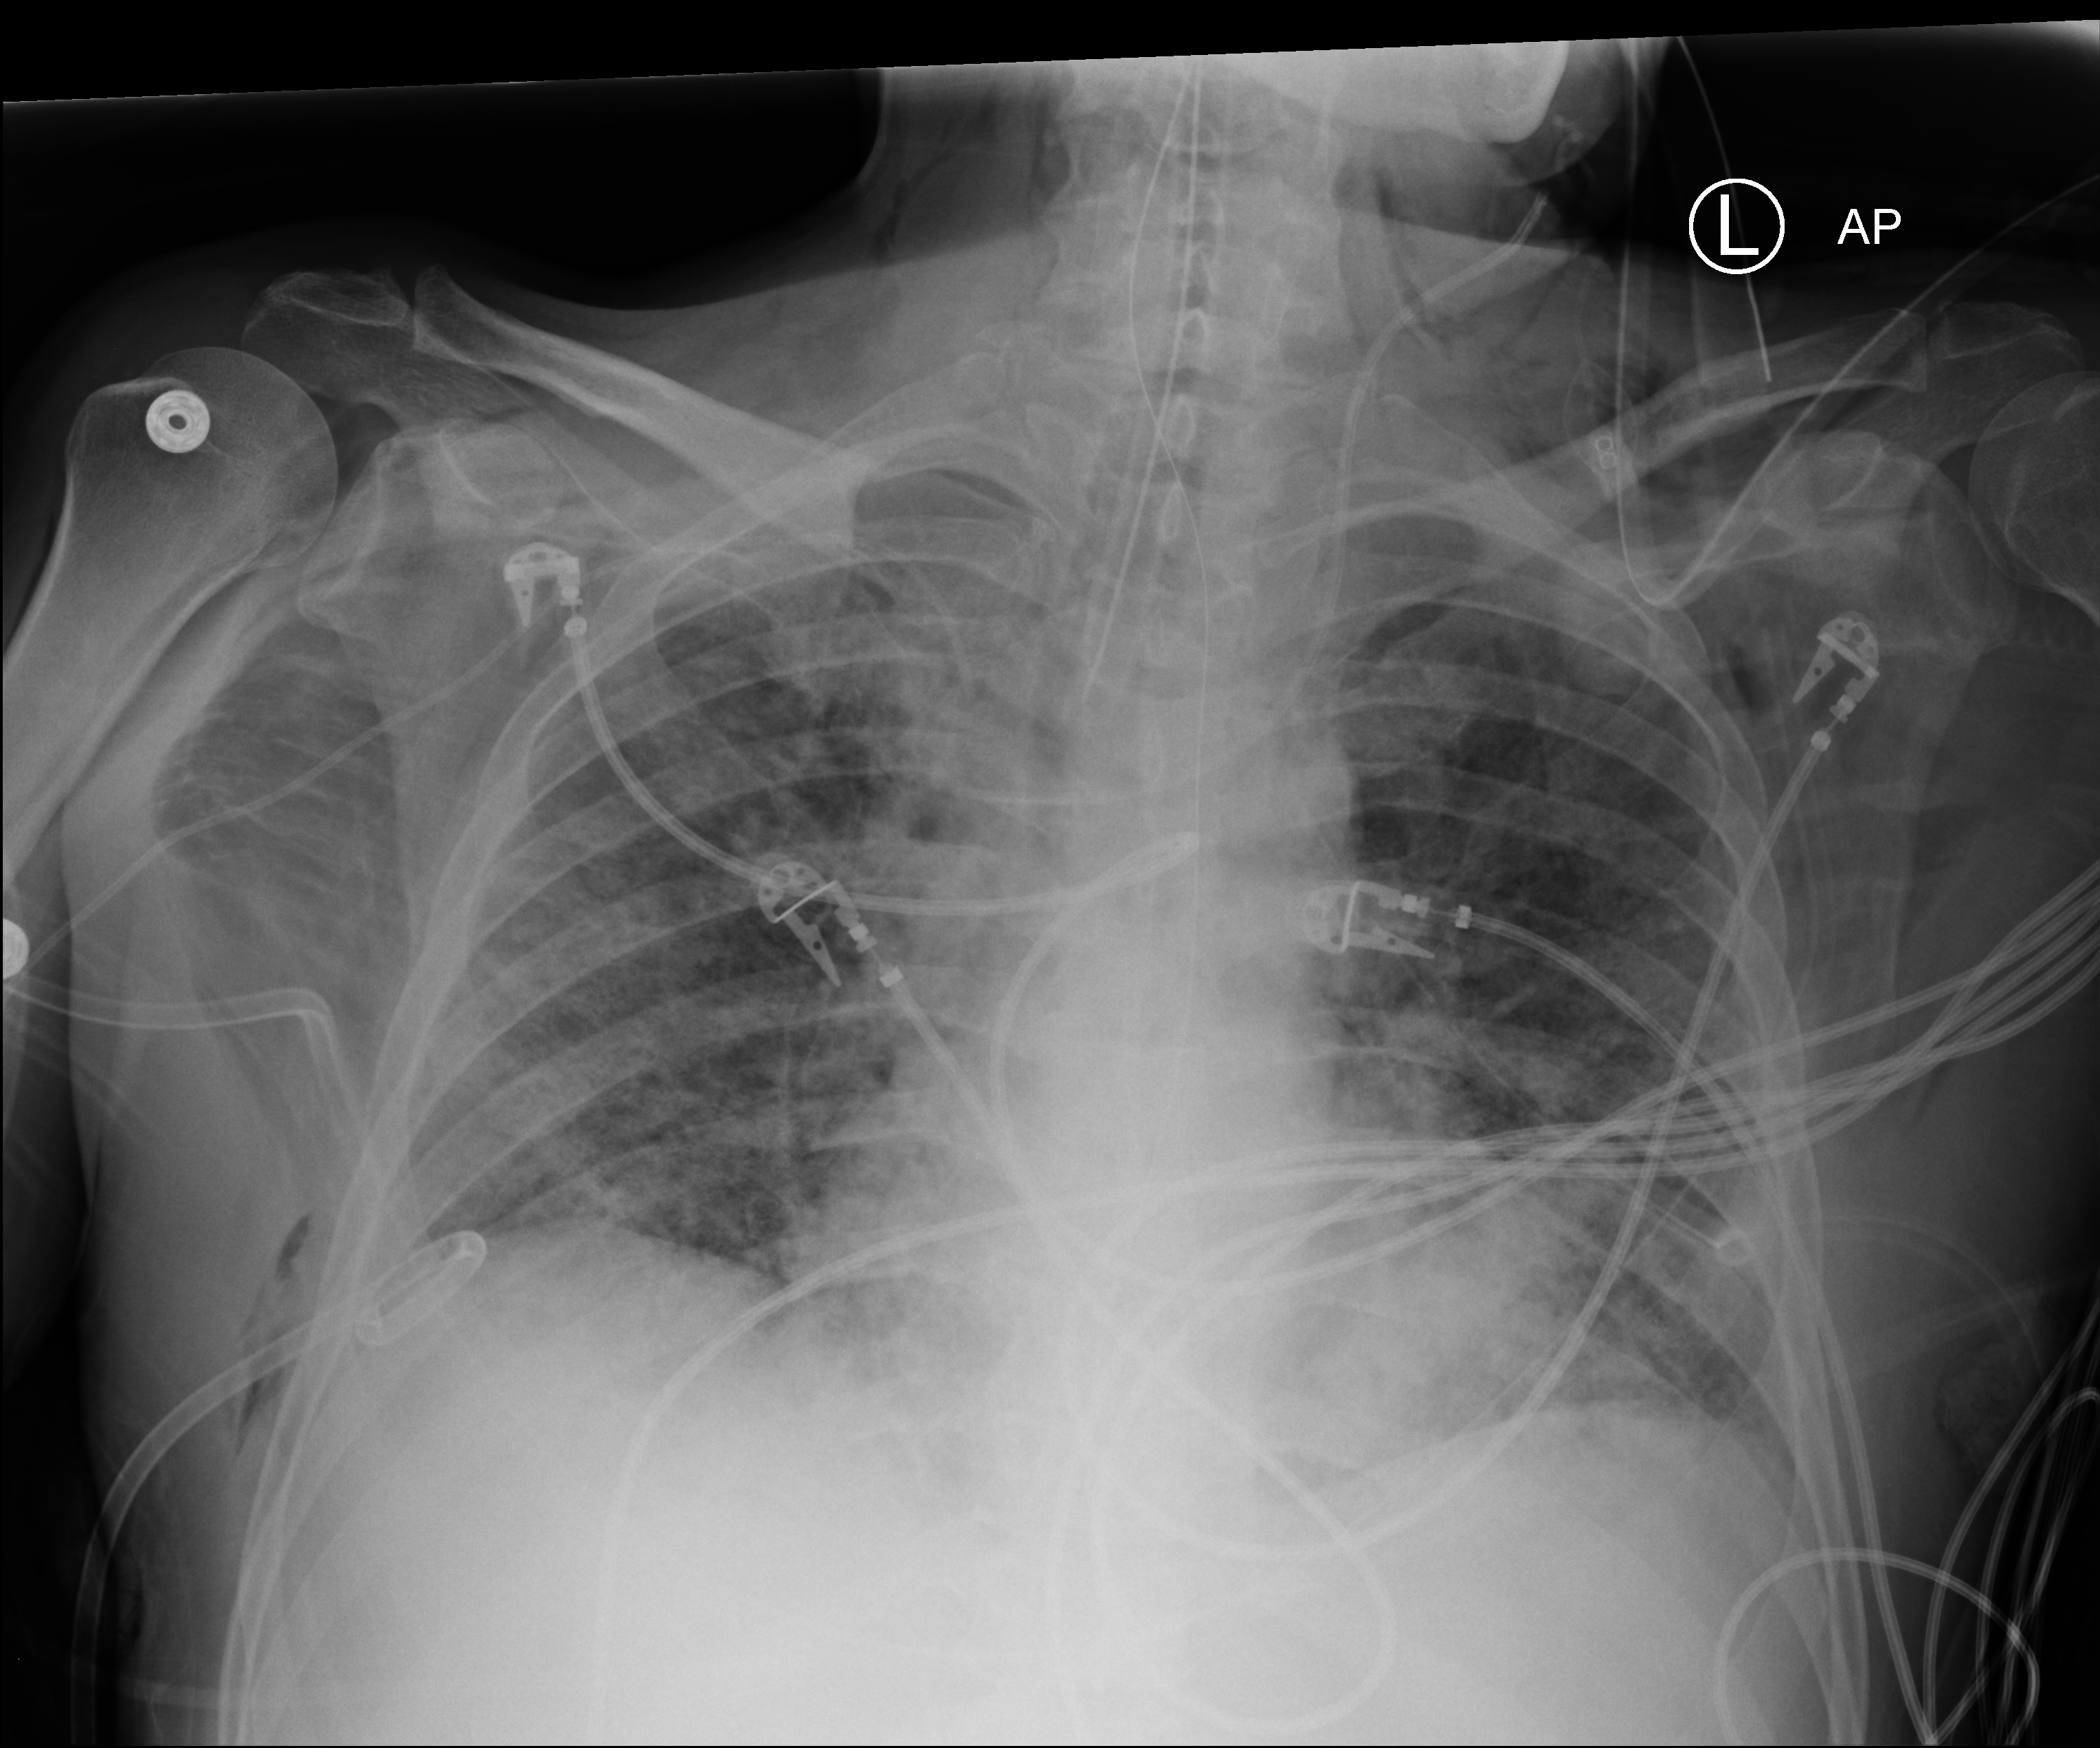
Bedside chest radiograph (computed radiography). Male patient hospitalised with COVID-19, age 18–59 years.
From the hospital-stay record, not from the radiograph (when in the stay this image was taken is not recorded): mechanically ventilated during this hospital stay: yes; diabetes (admission record): no; admitted to intensive care during this hospital stay: yes.